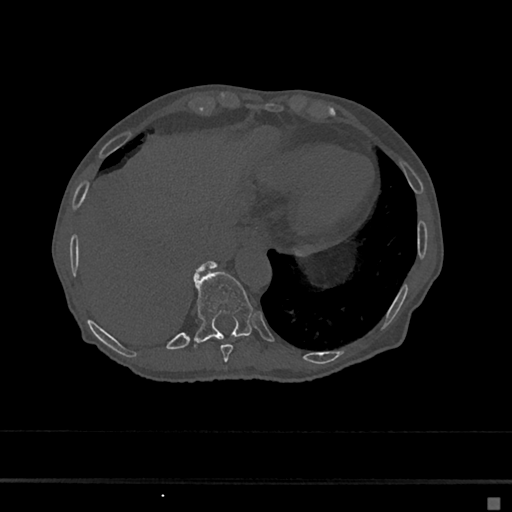
CT including the spine, one axial slice. Position 238 of 797 along the scan axis. 120 kVp. Bone window (W 1800 / L 400 HU). 512 × 512 image matrix, field of view 360 × 360 mm. Patient: female, 68 years. From the clinical record (not read from this slice): primary cancer: renal.
Annotated regions visible in this slice (semi-automatically segmented with operator editing):
- T10 vertebra: bounding box <194,266,254,343> (left, top, right, bottom; pixels)
- T11 vertebra: <195,262,216,275>
- T9 vertebra: <220,344,234,362>